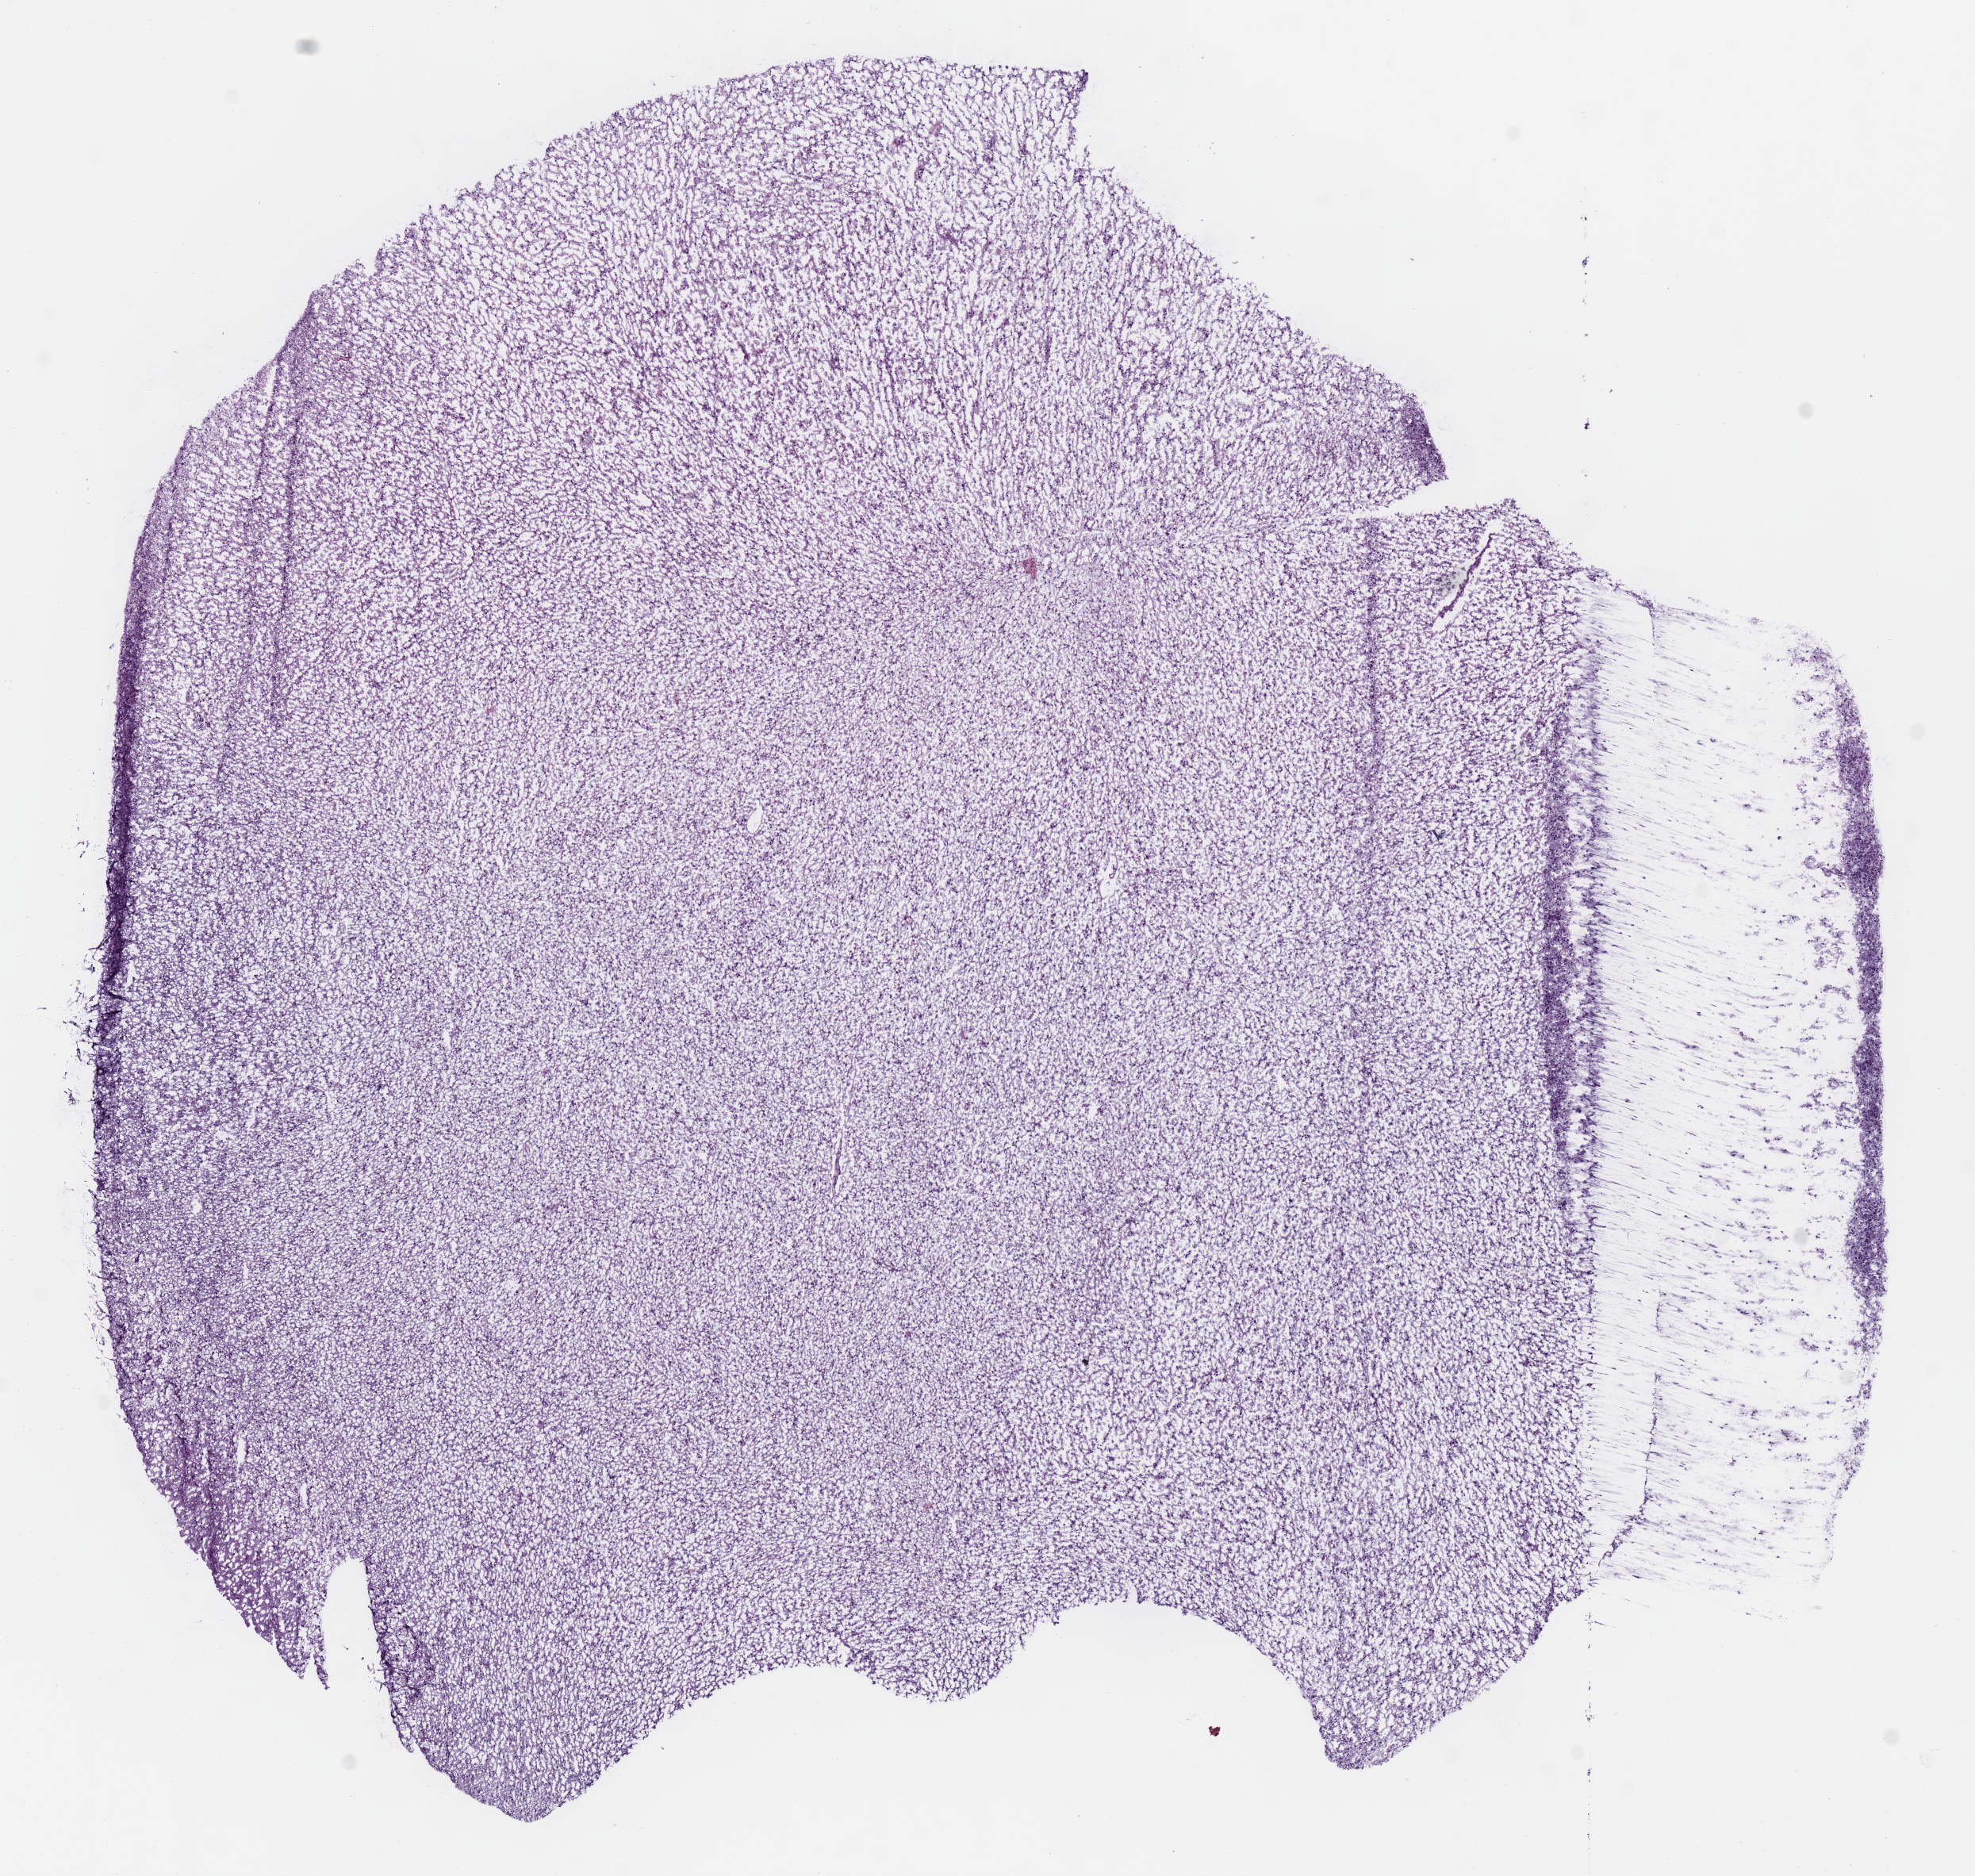
Digitized H&E tissue section (whole slide) — a low-resolution overview of the entire scanned area, about 9.8 x 9.3 mm (slide scanned at 40x), frozen section from the bottom of the tissue portion, sample: primary tumour, brain. Female, age 37 years at initial diagnosis.
Diagnosis: Mixed glioma (cerebrum).